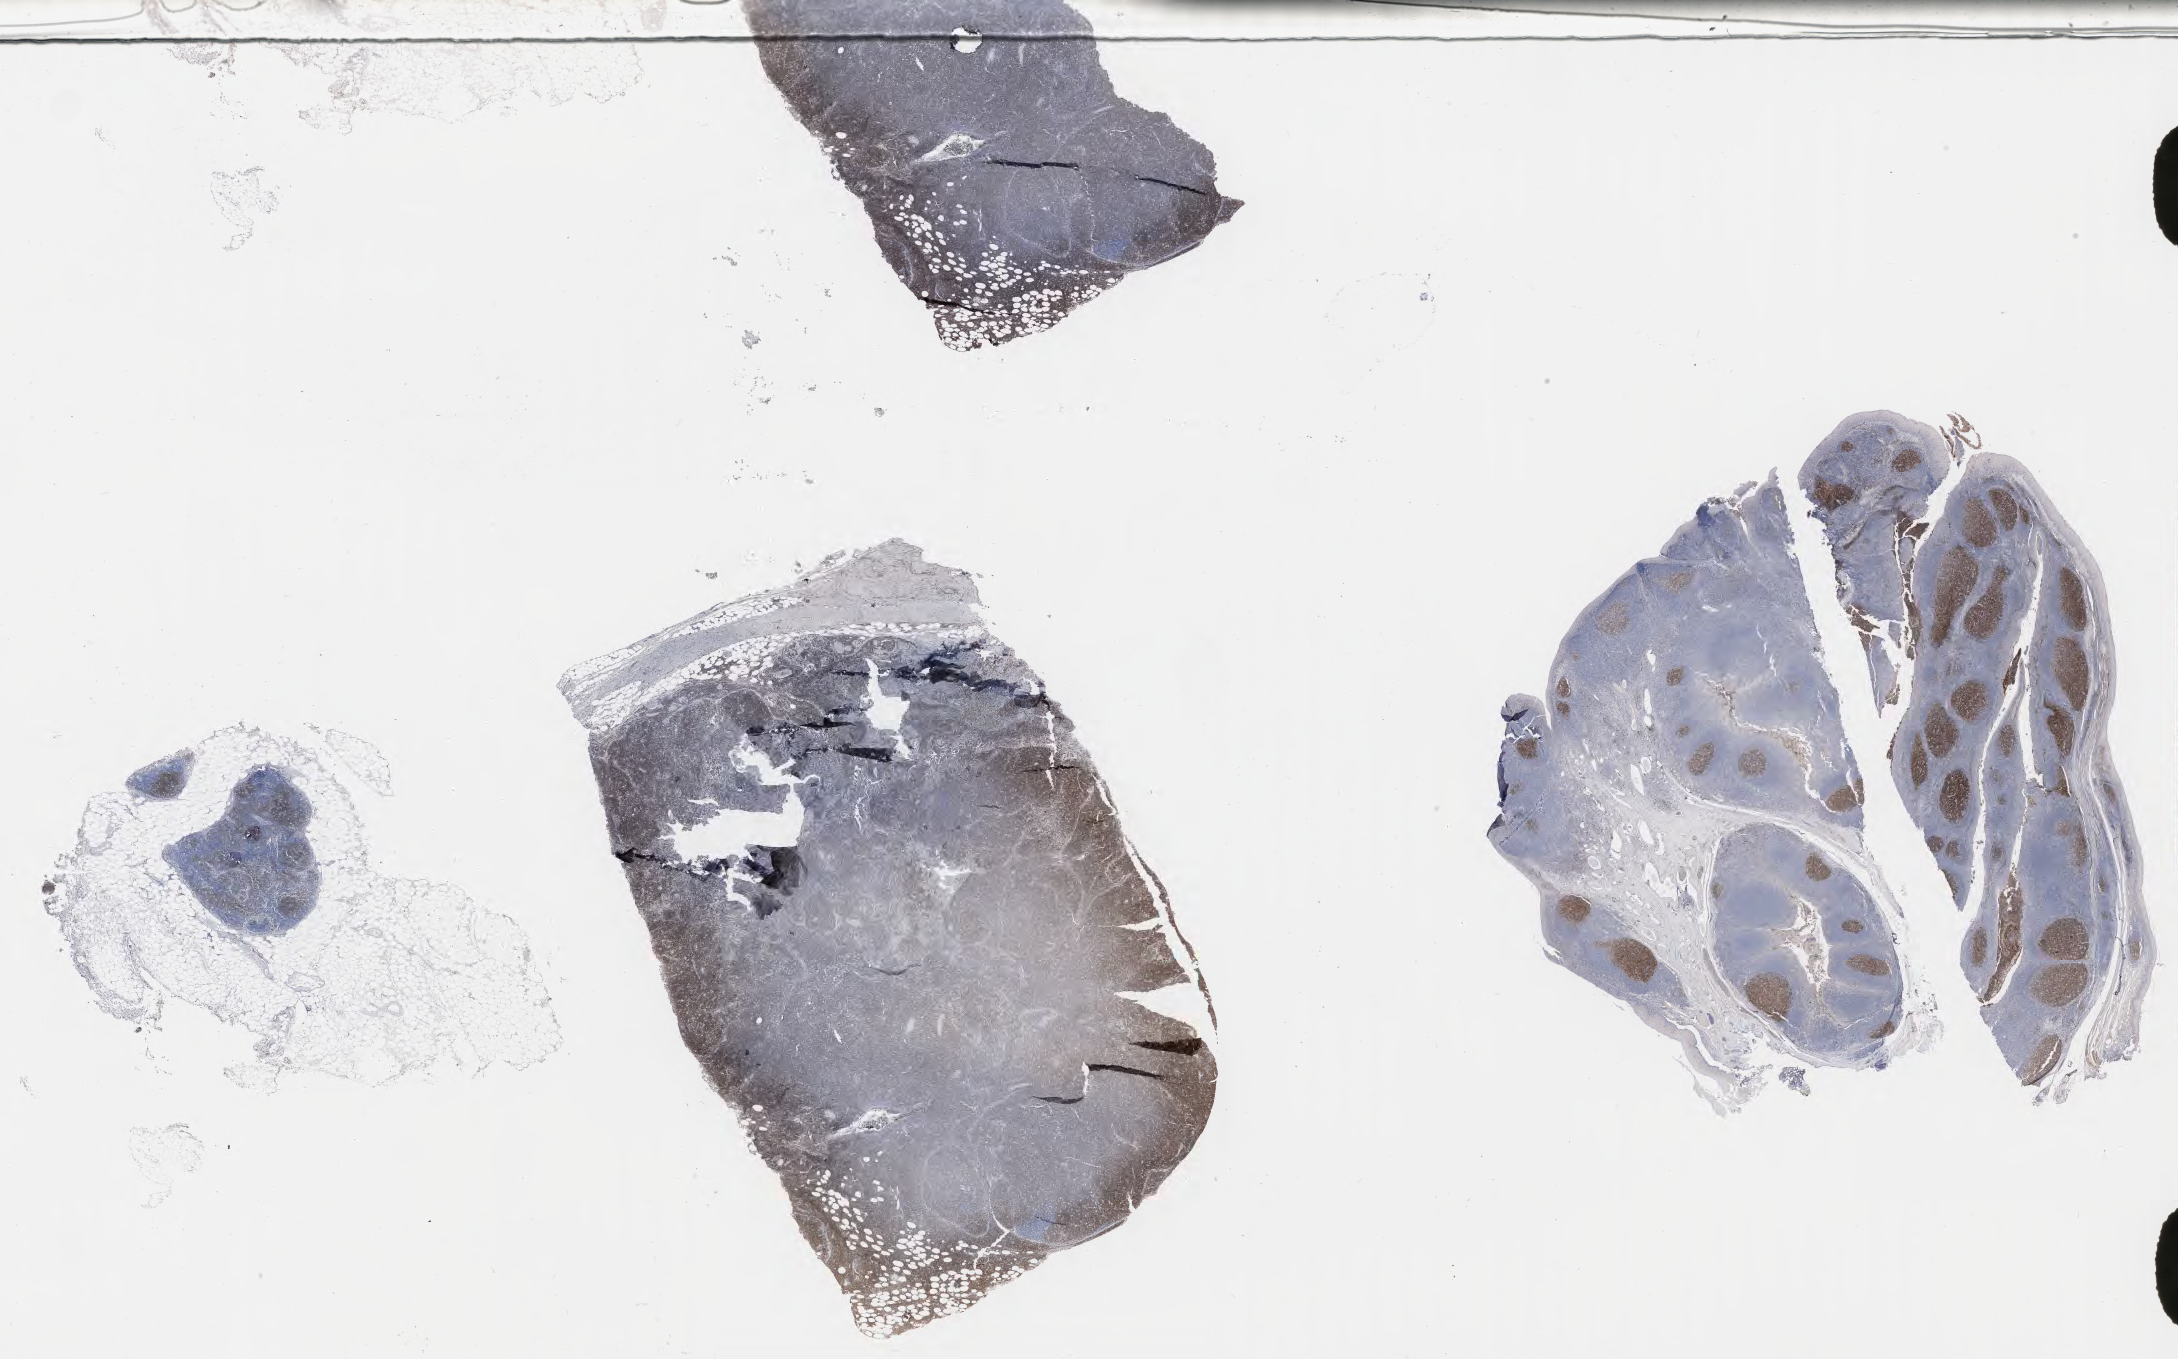
IHC for CD10, whole-slide image — a low-resolution overview of the entire scanned area, about 35.2 x 22.0 mm. Tumor tissue. Patient: male, 40 years old.
• histologic diagnosis: Burkitt lymphoma, NOS